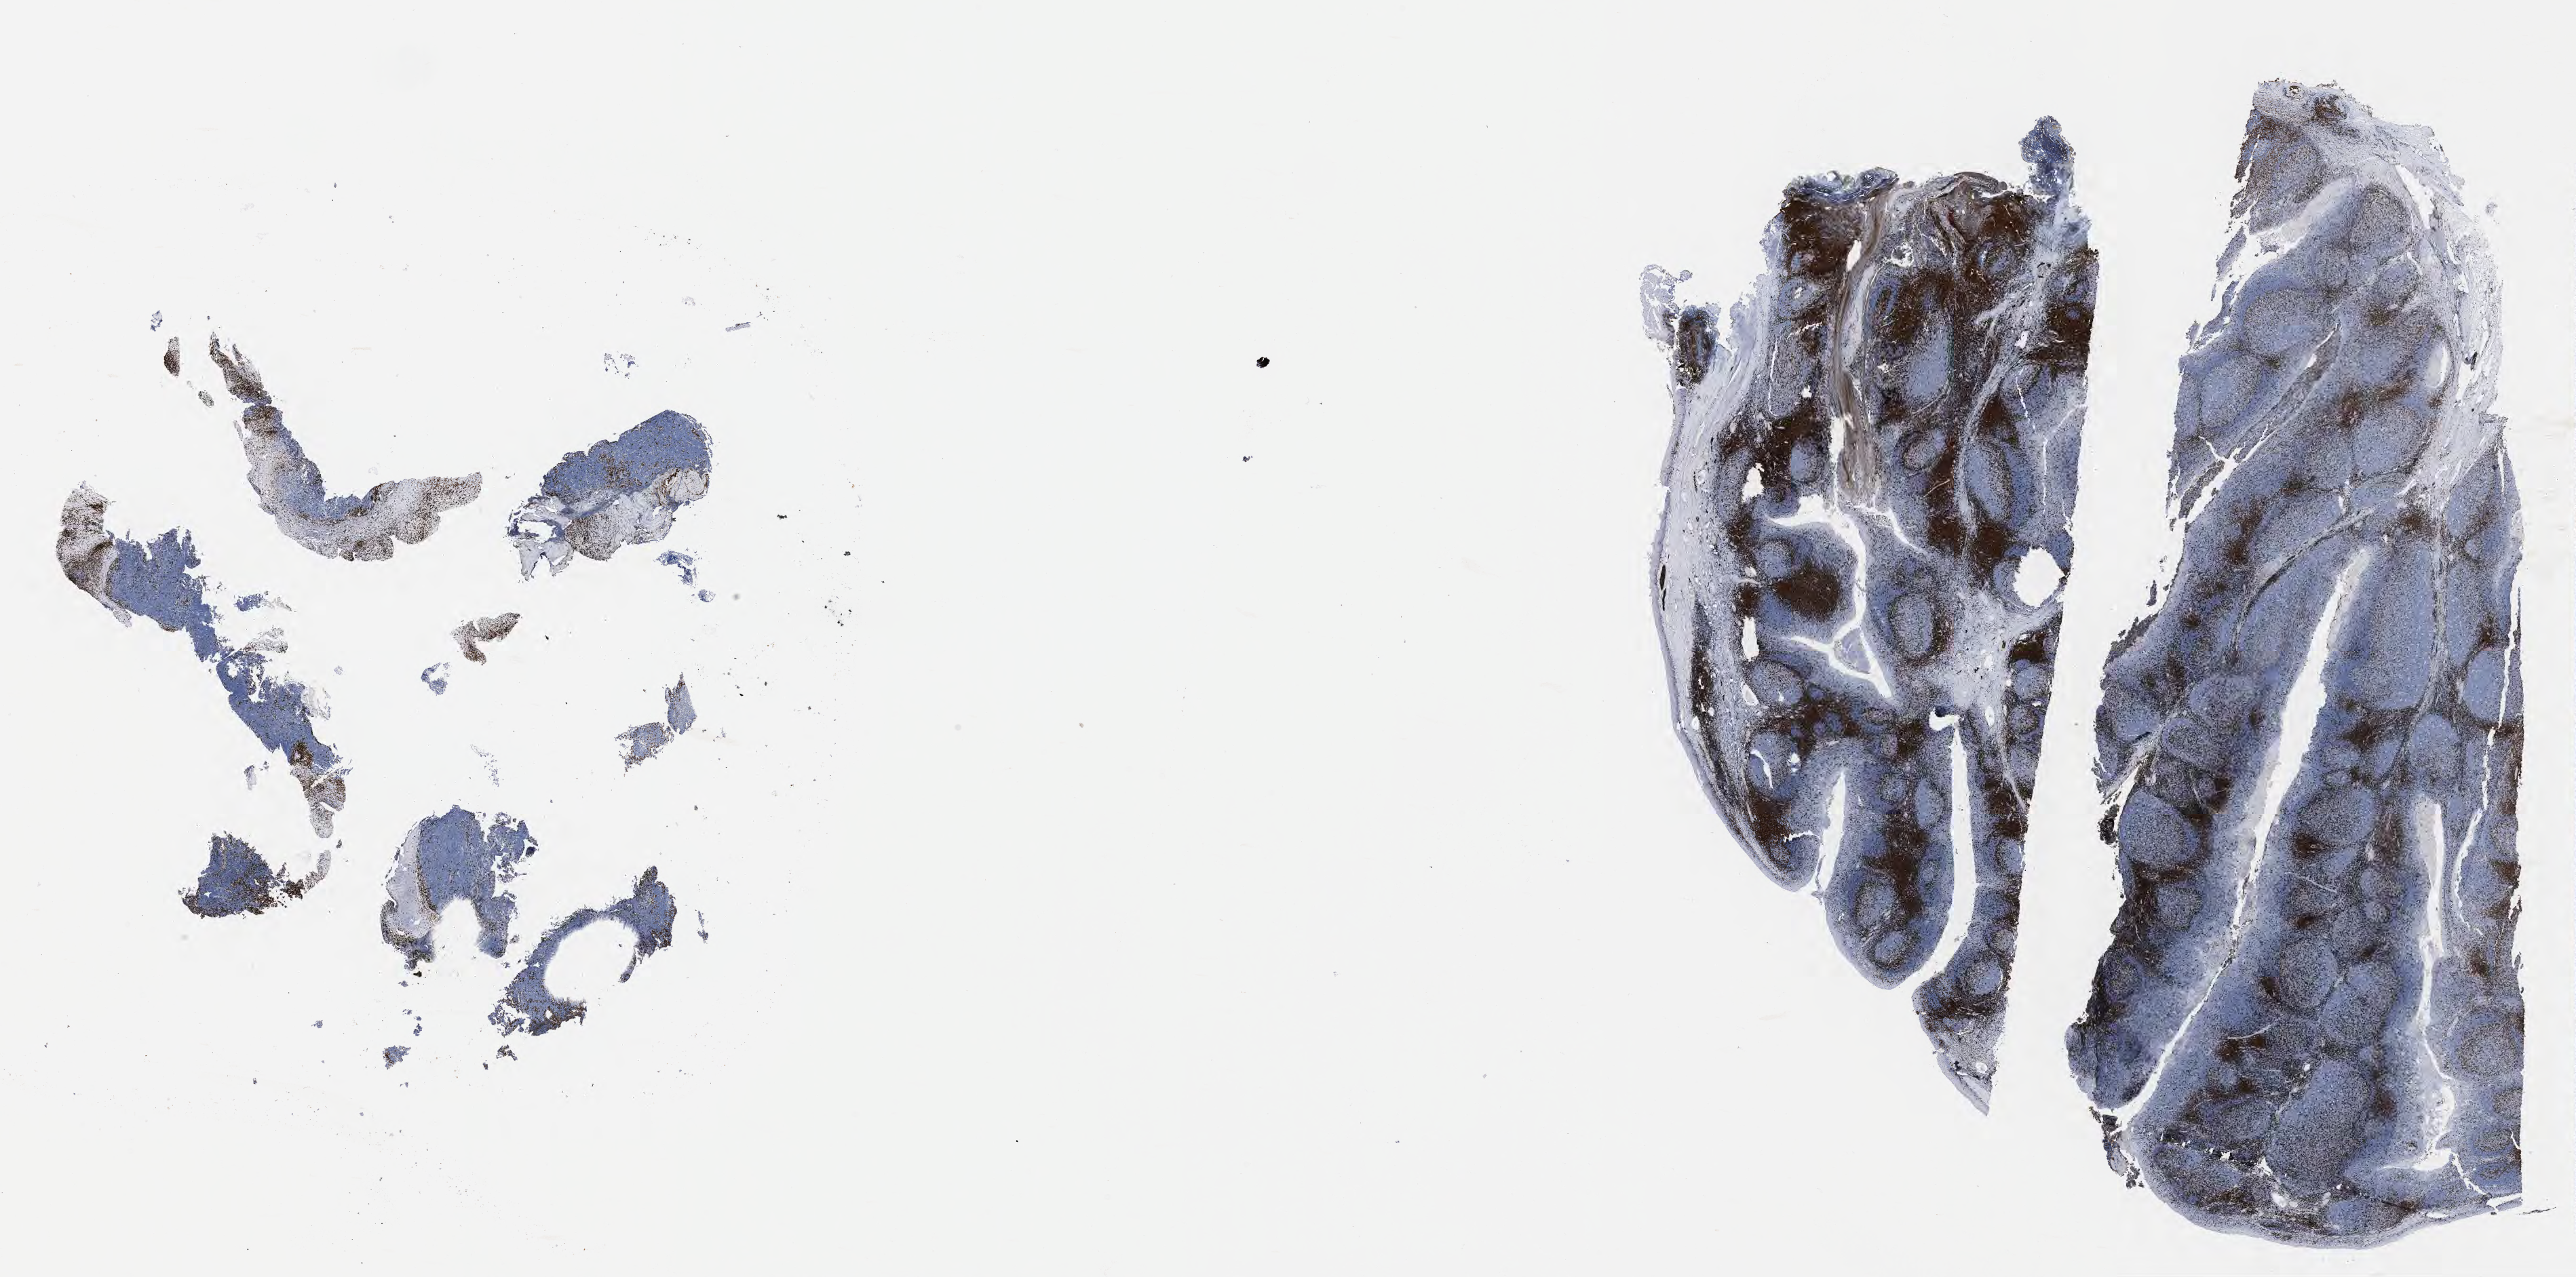
Whole-slide image, immunohistochemical stain for CD3 — low-resolution overview of the scanned area, about 30.7 x 15.2 mm. Tumor tissue. Patient: female, age at initial diagnosis 9 years.
Histologic diagnosis: Burkitt lymphoma, NOS.